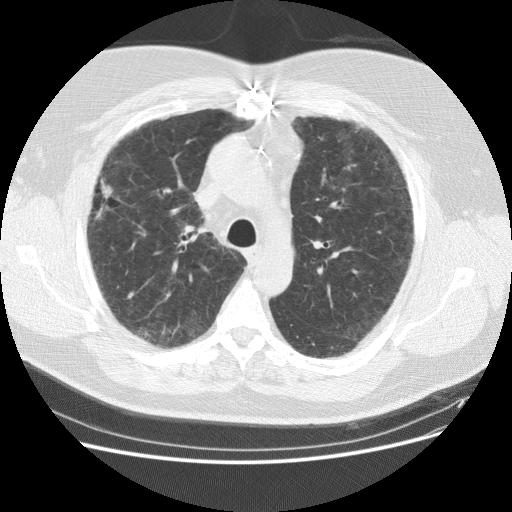
Low-dose screening chest CT, one axial slice; slice 112 of 151 in the series (ordered by position); reconstruction kernel STANDARD; 120 kVp; lung window (W 1500 / L -600 HU); 512 × 512 image matrix, field of view 378 × 378 mm.
Structures marked on this image (outlined manually by an expert reader):
- lesion 2 (tumor, upper lobe of right lung): box from (x=99, y=182) to (x=117, y=202) px